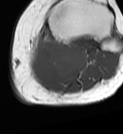
MRI of an extremity soft-tissue mass, one axial slice. Slice 44 of 68 in the series (ordered by position). MR volume resampled by the dataset authors to the PET/CT grid (not the native acquisition matrix). 3.27 mm slice thickness. 123 × 134 image matrix, field of view 120 × 131 mm. Female patient. From the clinical record (not read from this slice): histological type: extraskeletal high grade osteogenic sarcoma; grade: high; site of the primary tumour: left calf.
Outlined on this slice (expert contour drawn on MRI and transferred to this co-registered scan by the dataset authors):
- gross tumour volume (mass): box from (x=28, y=39) to (x=89, y=86) px